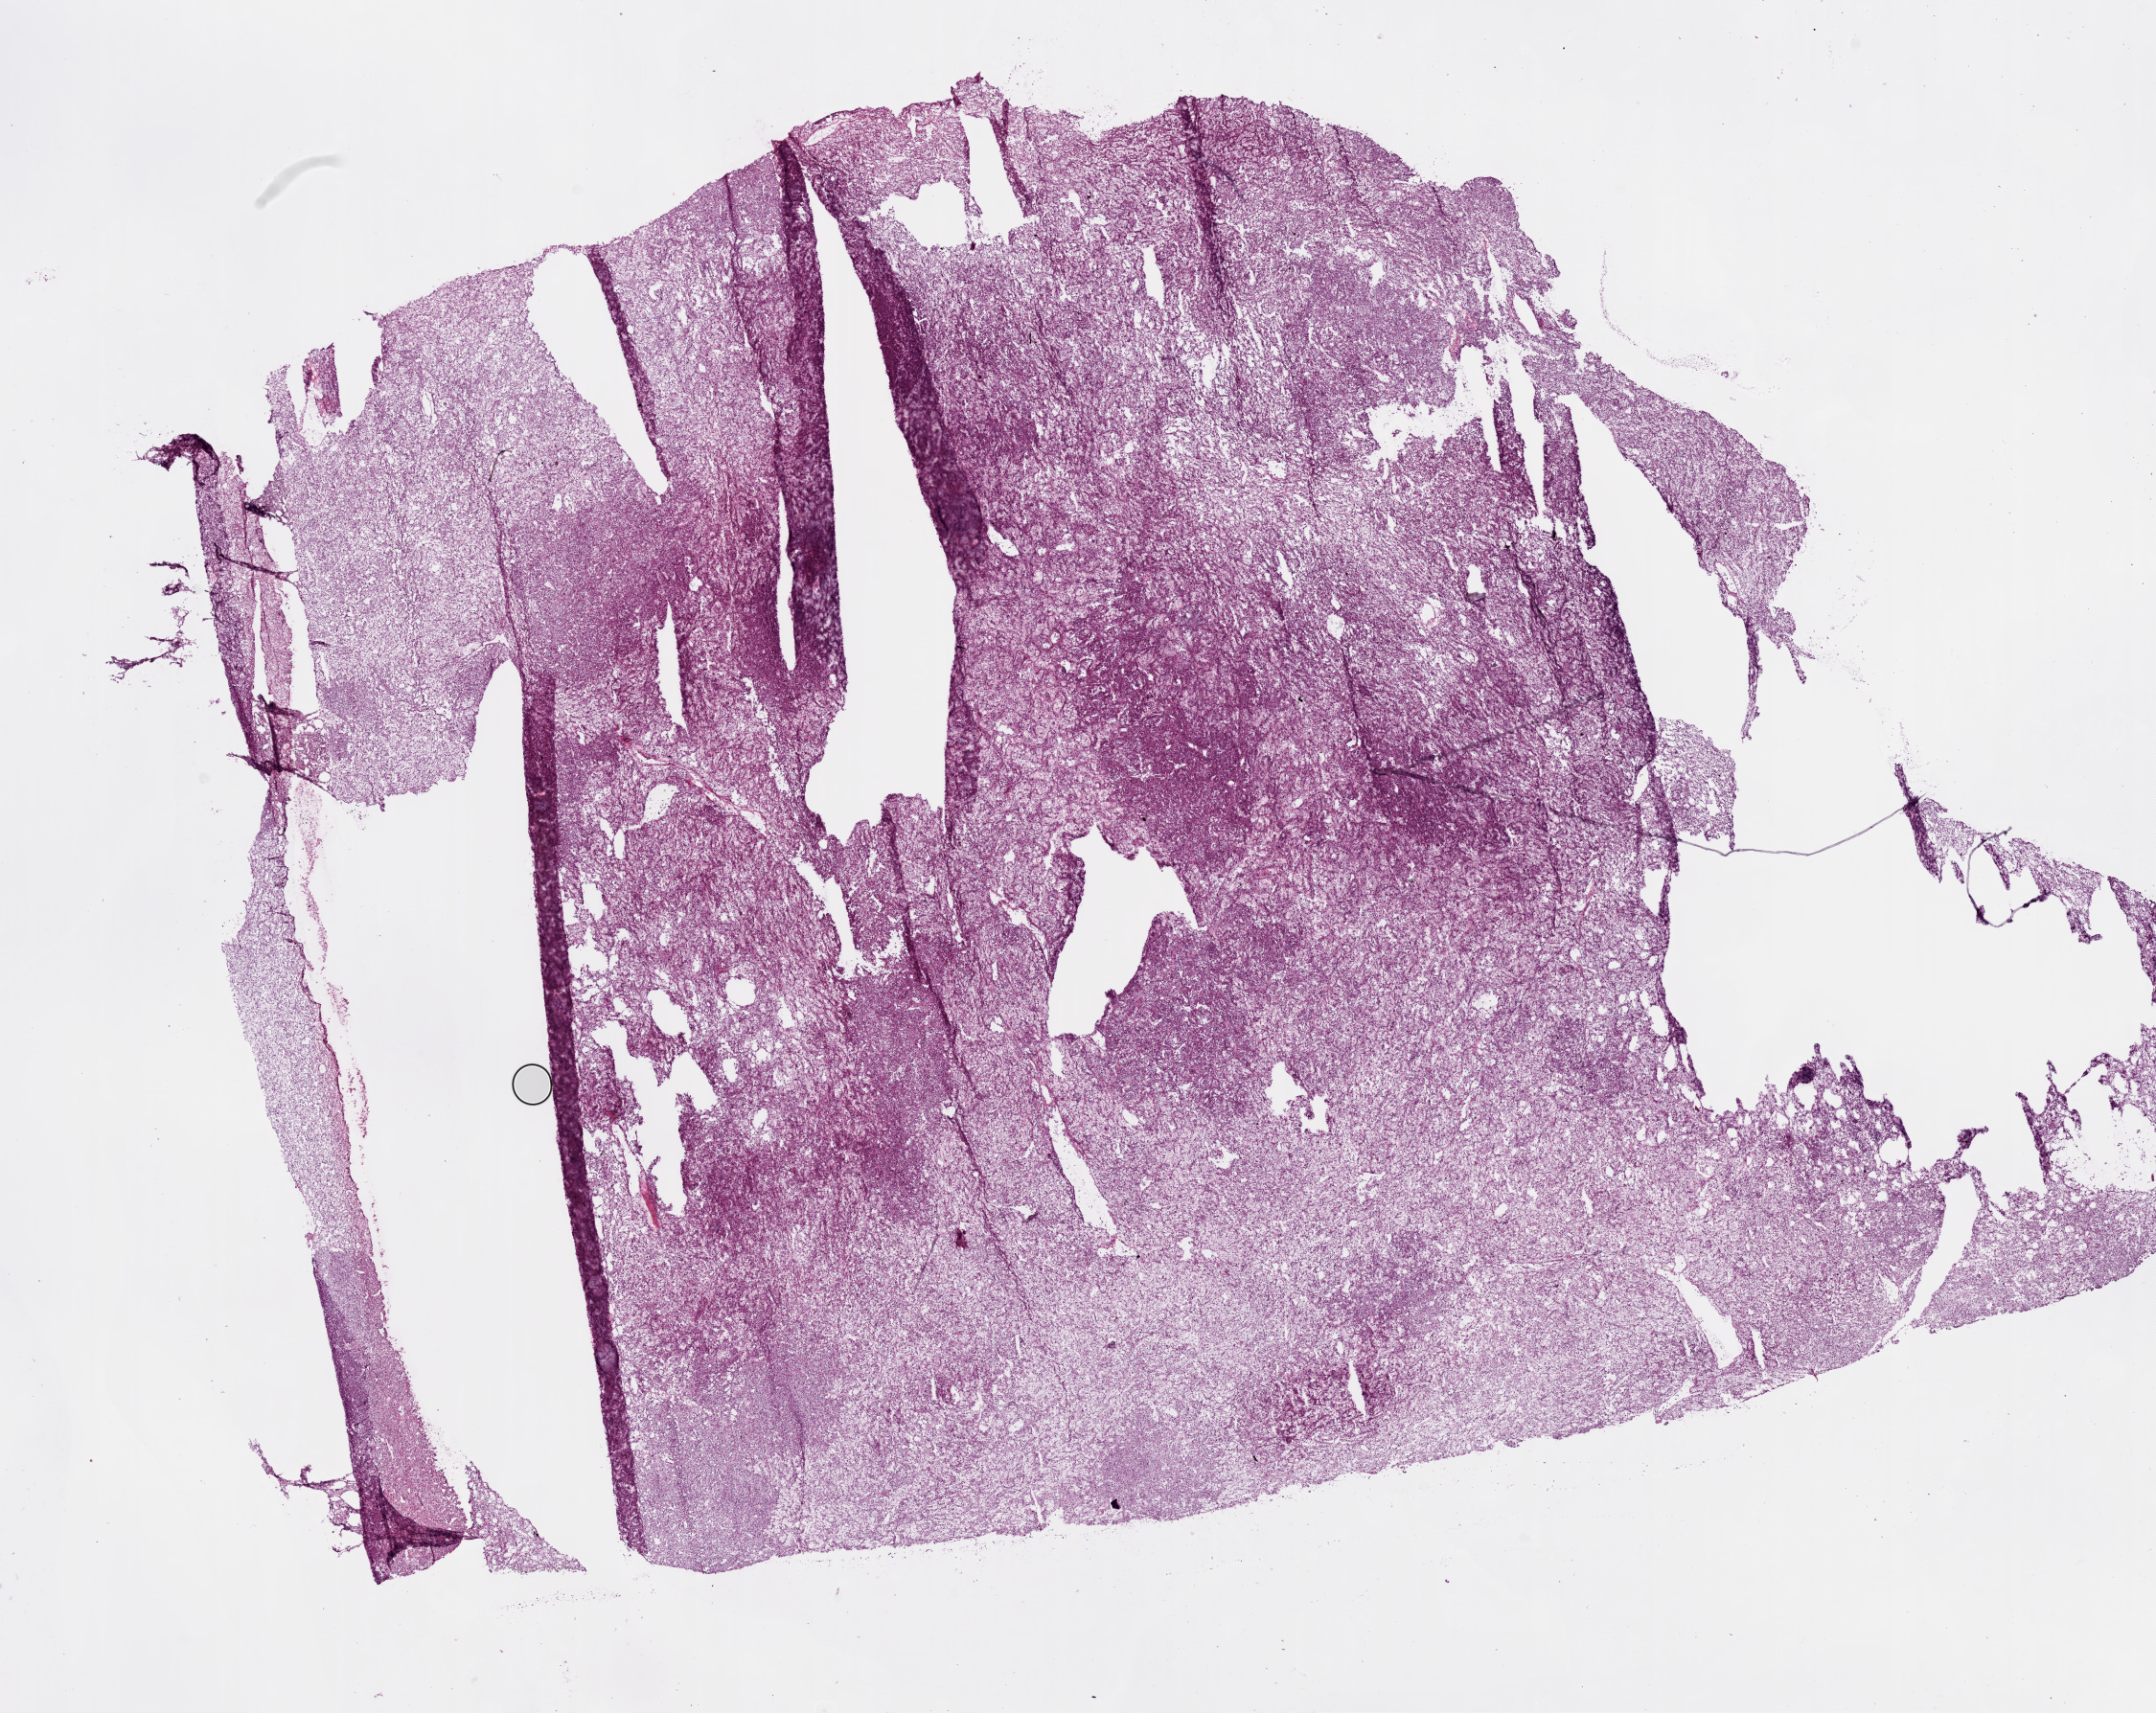
Whole-slide histology image, Hematoxylin and eosin (H&E) stained — a low-resolution overview of the entire scanned area, about 18.1 x 14.3 mm (from a 20x scan). Frozen section from the bottom of the tissue portion. Sample: primary tumour, kidney. Male patient; age at initial diagnosis 77 years. Histologic grade: G3 (poorly differentiated). Slide review estimates, as recorded: tumour cells 95%, tumour nuclei 85%, normal cells 0%, stromal cells 5%, necrosis 0%.
Diagnosis: Clear cell adenocarcinoma, NOS. AJCC pathologic stage: I (6th edition).